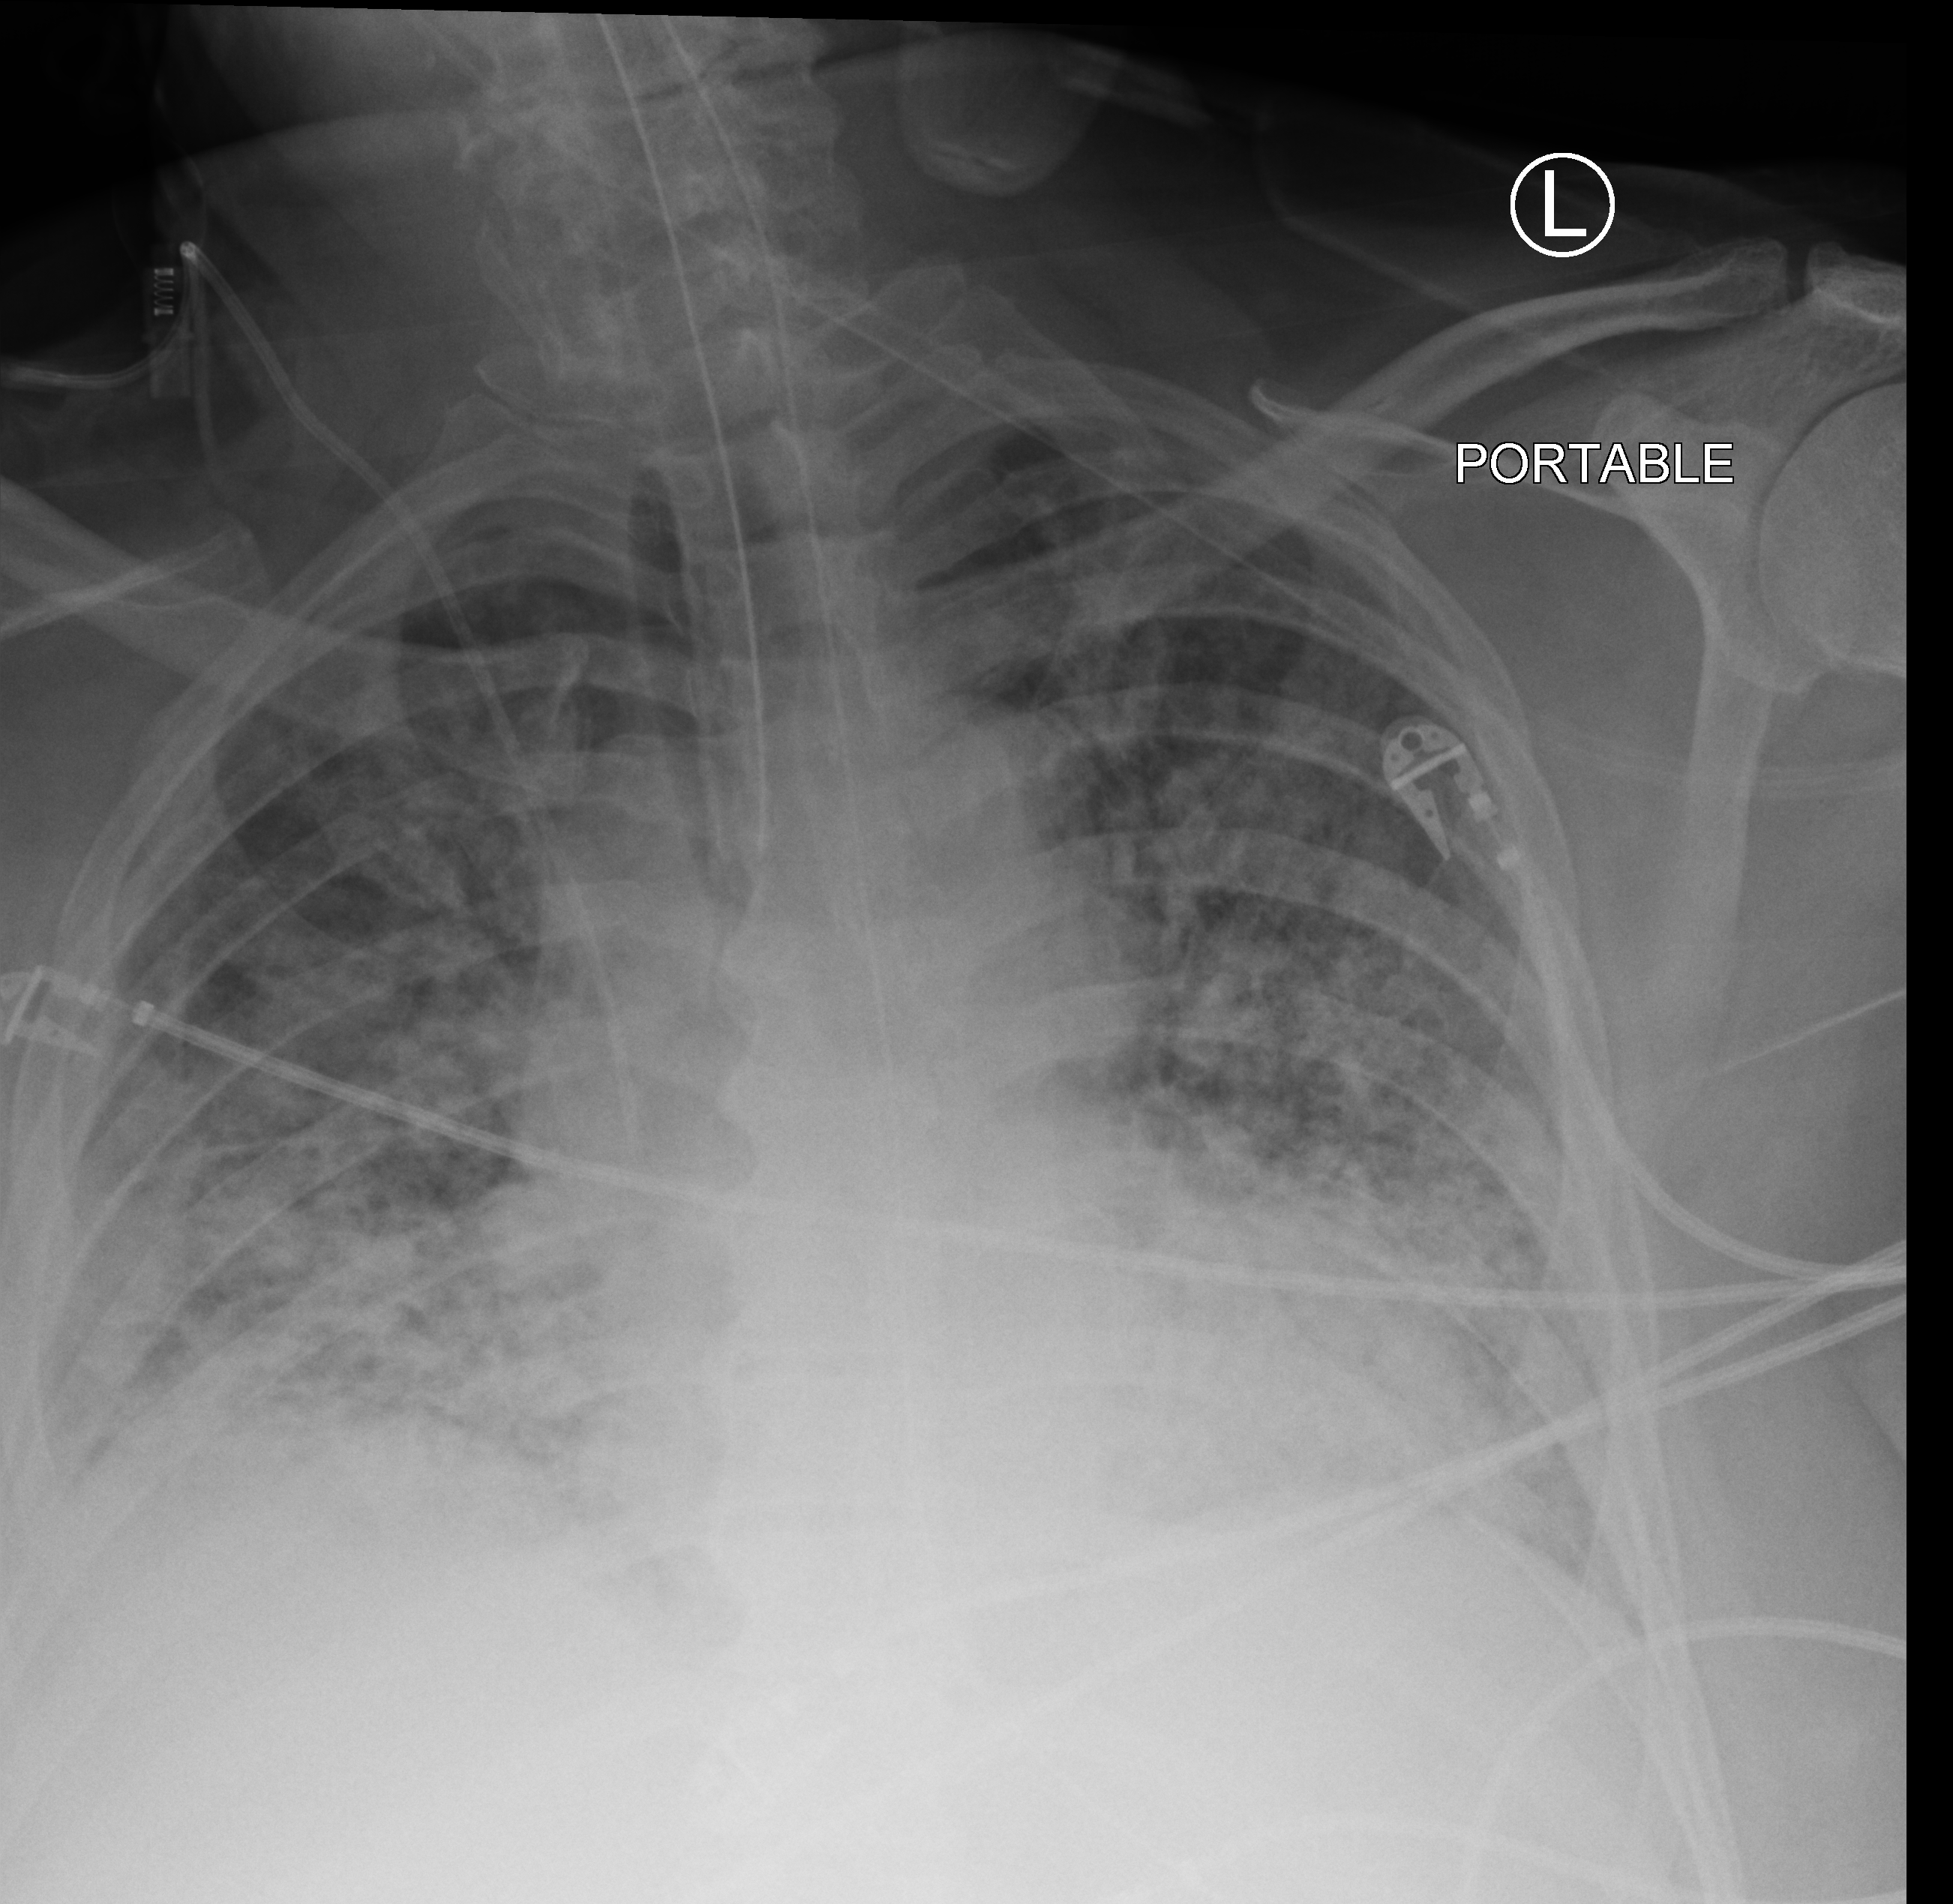
Chest X-ray (portable). Male patient hospitalised with COVID-19, age 60–74 years.
Admission-level facts for this patient (not findings on this image; timing relative to this image not recorded):
- admitted to intensive care during this hospital stay: yes
- COPD (admission record): no
- hypertension (admission record): yes